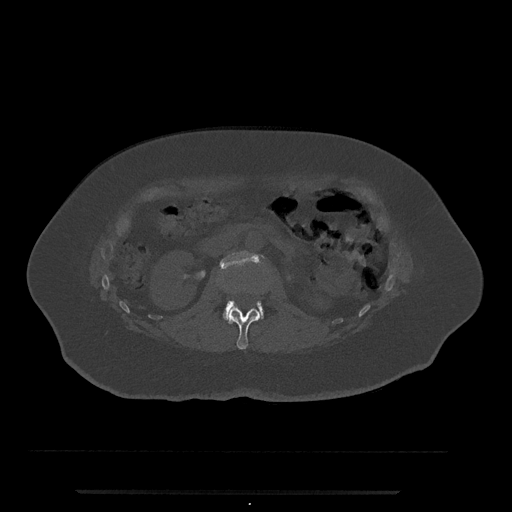
CT including the spine, one axial slice. Position 72 of 797 along the scan axis. Reconstruction kernel Br40s/3. 120 kVp. Bone window (W 1800 / L 400 HU). 512 × 512 image matrix, field of view 440 × 440 mm. Female patient, age 51 years. From the clinical record (not read from this slice): primary cancer: neuro; vertebrae with lytic lesions (as recorded): T8.
Annotated regions visible in this slice (semi-automatic segmentation, software-assisted and operator-edited):
- L1 vertebra: bounding box [x1, y1, x2, y2] px = [223, 308, 262, 350]
- L2 vertebra: [220, 250, 264, 319]